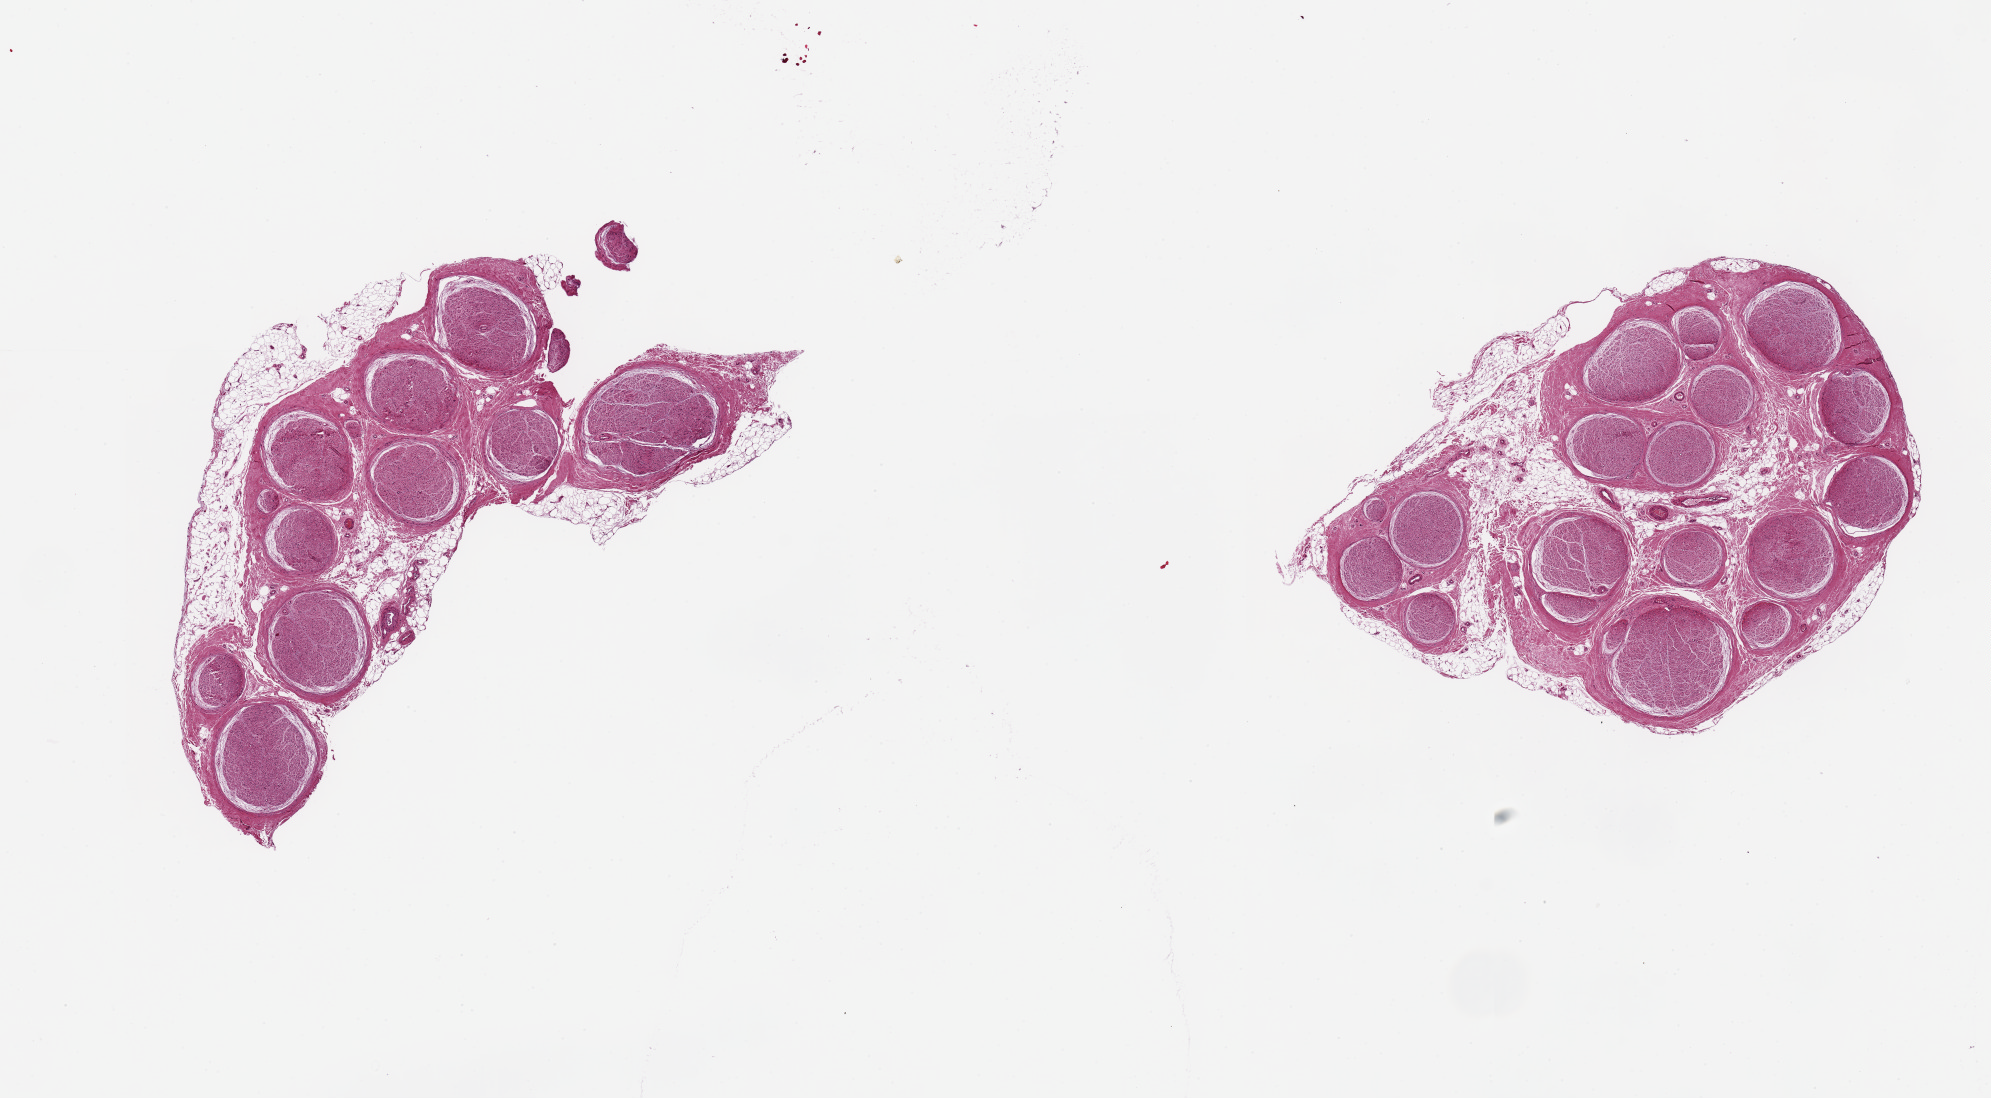
Whole-slide image, hematoxylin and eosin (H&E) stain, brightfield, low-resolution overview of the scanned area, about 15.8 x 8.7 mm. PAXgene-fixed paraffin-embedded (PFPE) section. Sampled site (target tissue): tibial nerve. Donor tissue sample. Donor: male.
Review note (as recorded): 2 pieces, 6x5 & 5x4mm; 10-20% adipose.